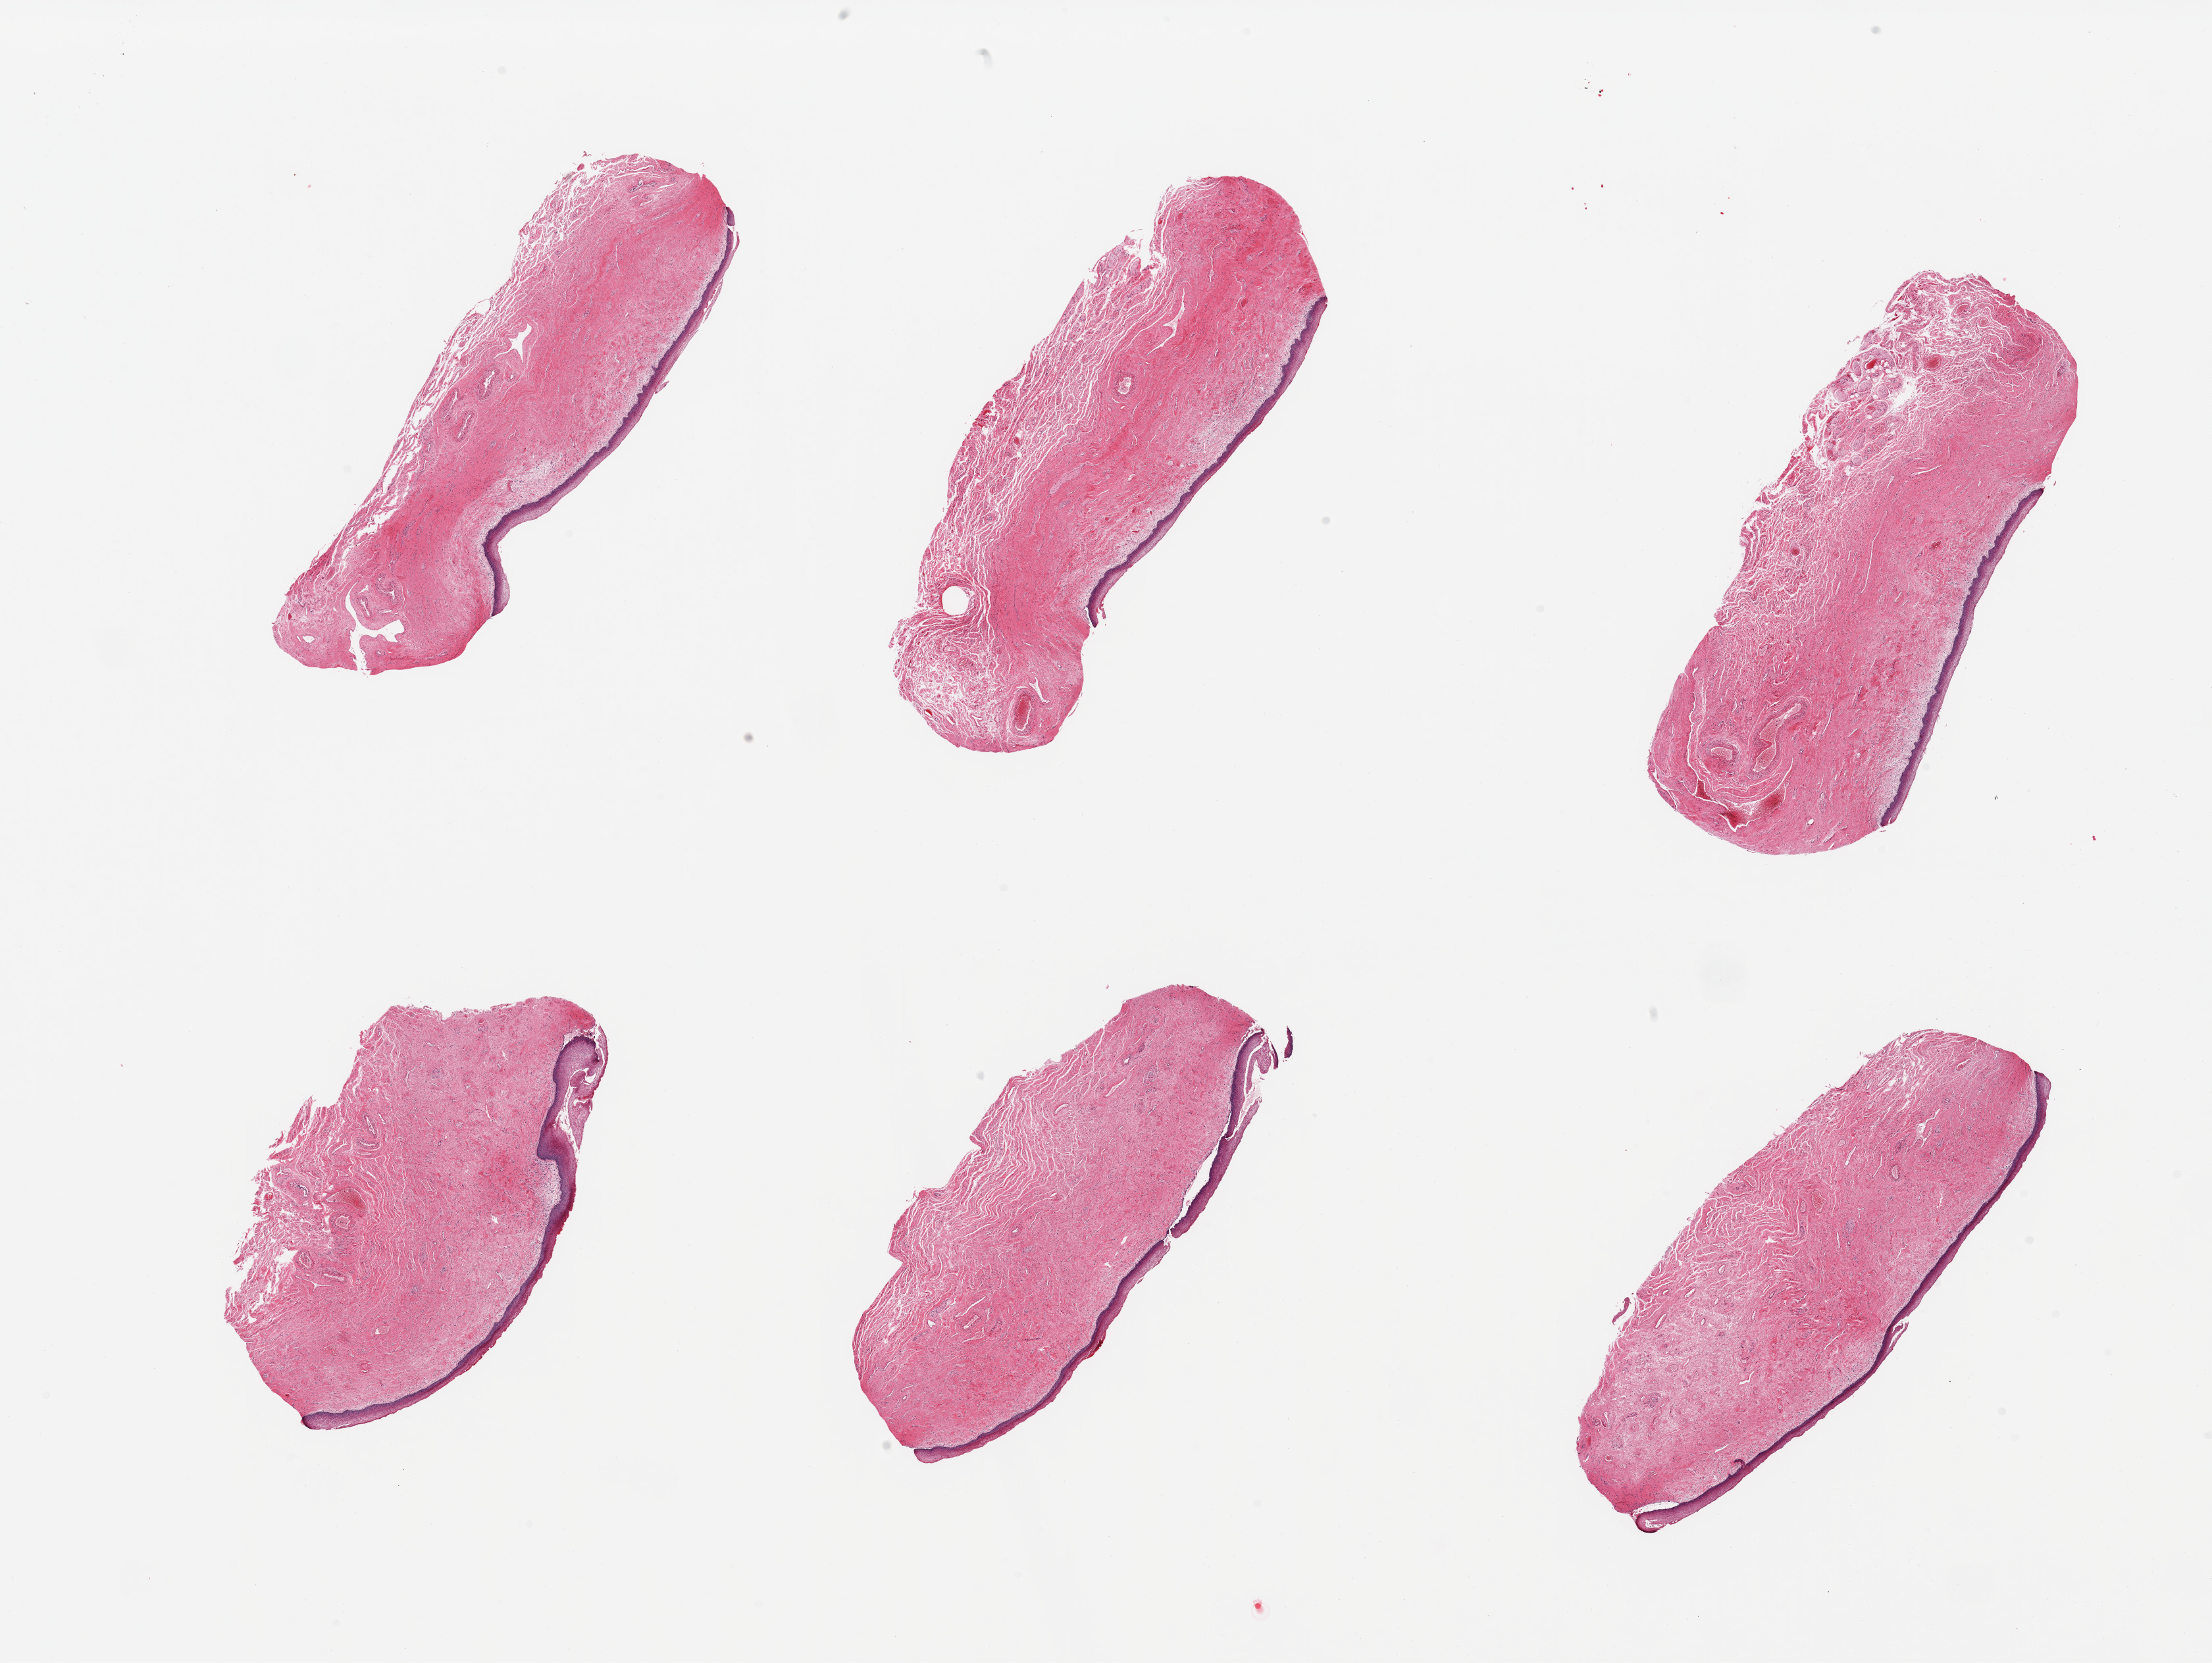
Whole-slide image, hematoxylin and eosin (H&E) stain, low-resolution overview of the scanned area, about 26.6 x 20.0 mm. PAXgene-fixed paraffin-embedded (PFPE) section. Target tissue: vagina. Donor tissue sample. Donor sex: female.
• review note (as recorded): 6 pieces, squamous mucosa sloughing